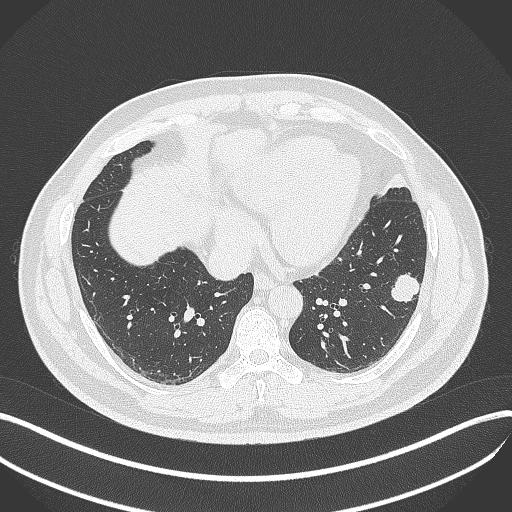
Chest CT, one axial slice; position 144 of 429 along the scan axis; 120 kVp; lung window (W 1500 / L -600 HU); 512 × 512 image matrix. Male patient, age 39 years. Case-level facts recorded for this patient, not image findings: clinical TNM (as recorded): T2a N0 M0.
Annotated regions visible in this slice (rectangle marked by the reading radiologist):
- lung tumour (recorded histology: adenocarcinoma): bounding box (x1, y1, x2, y2) in pixels: (387, 271, 424, 307)